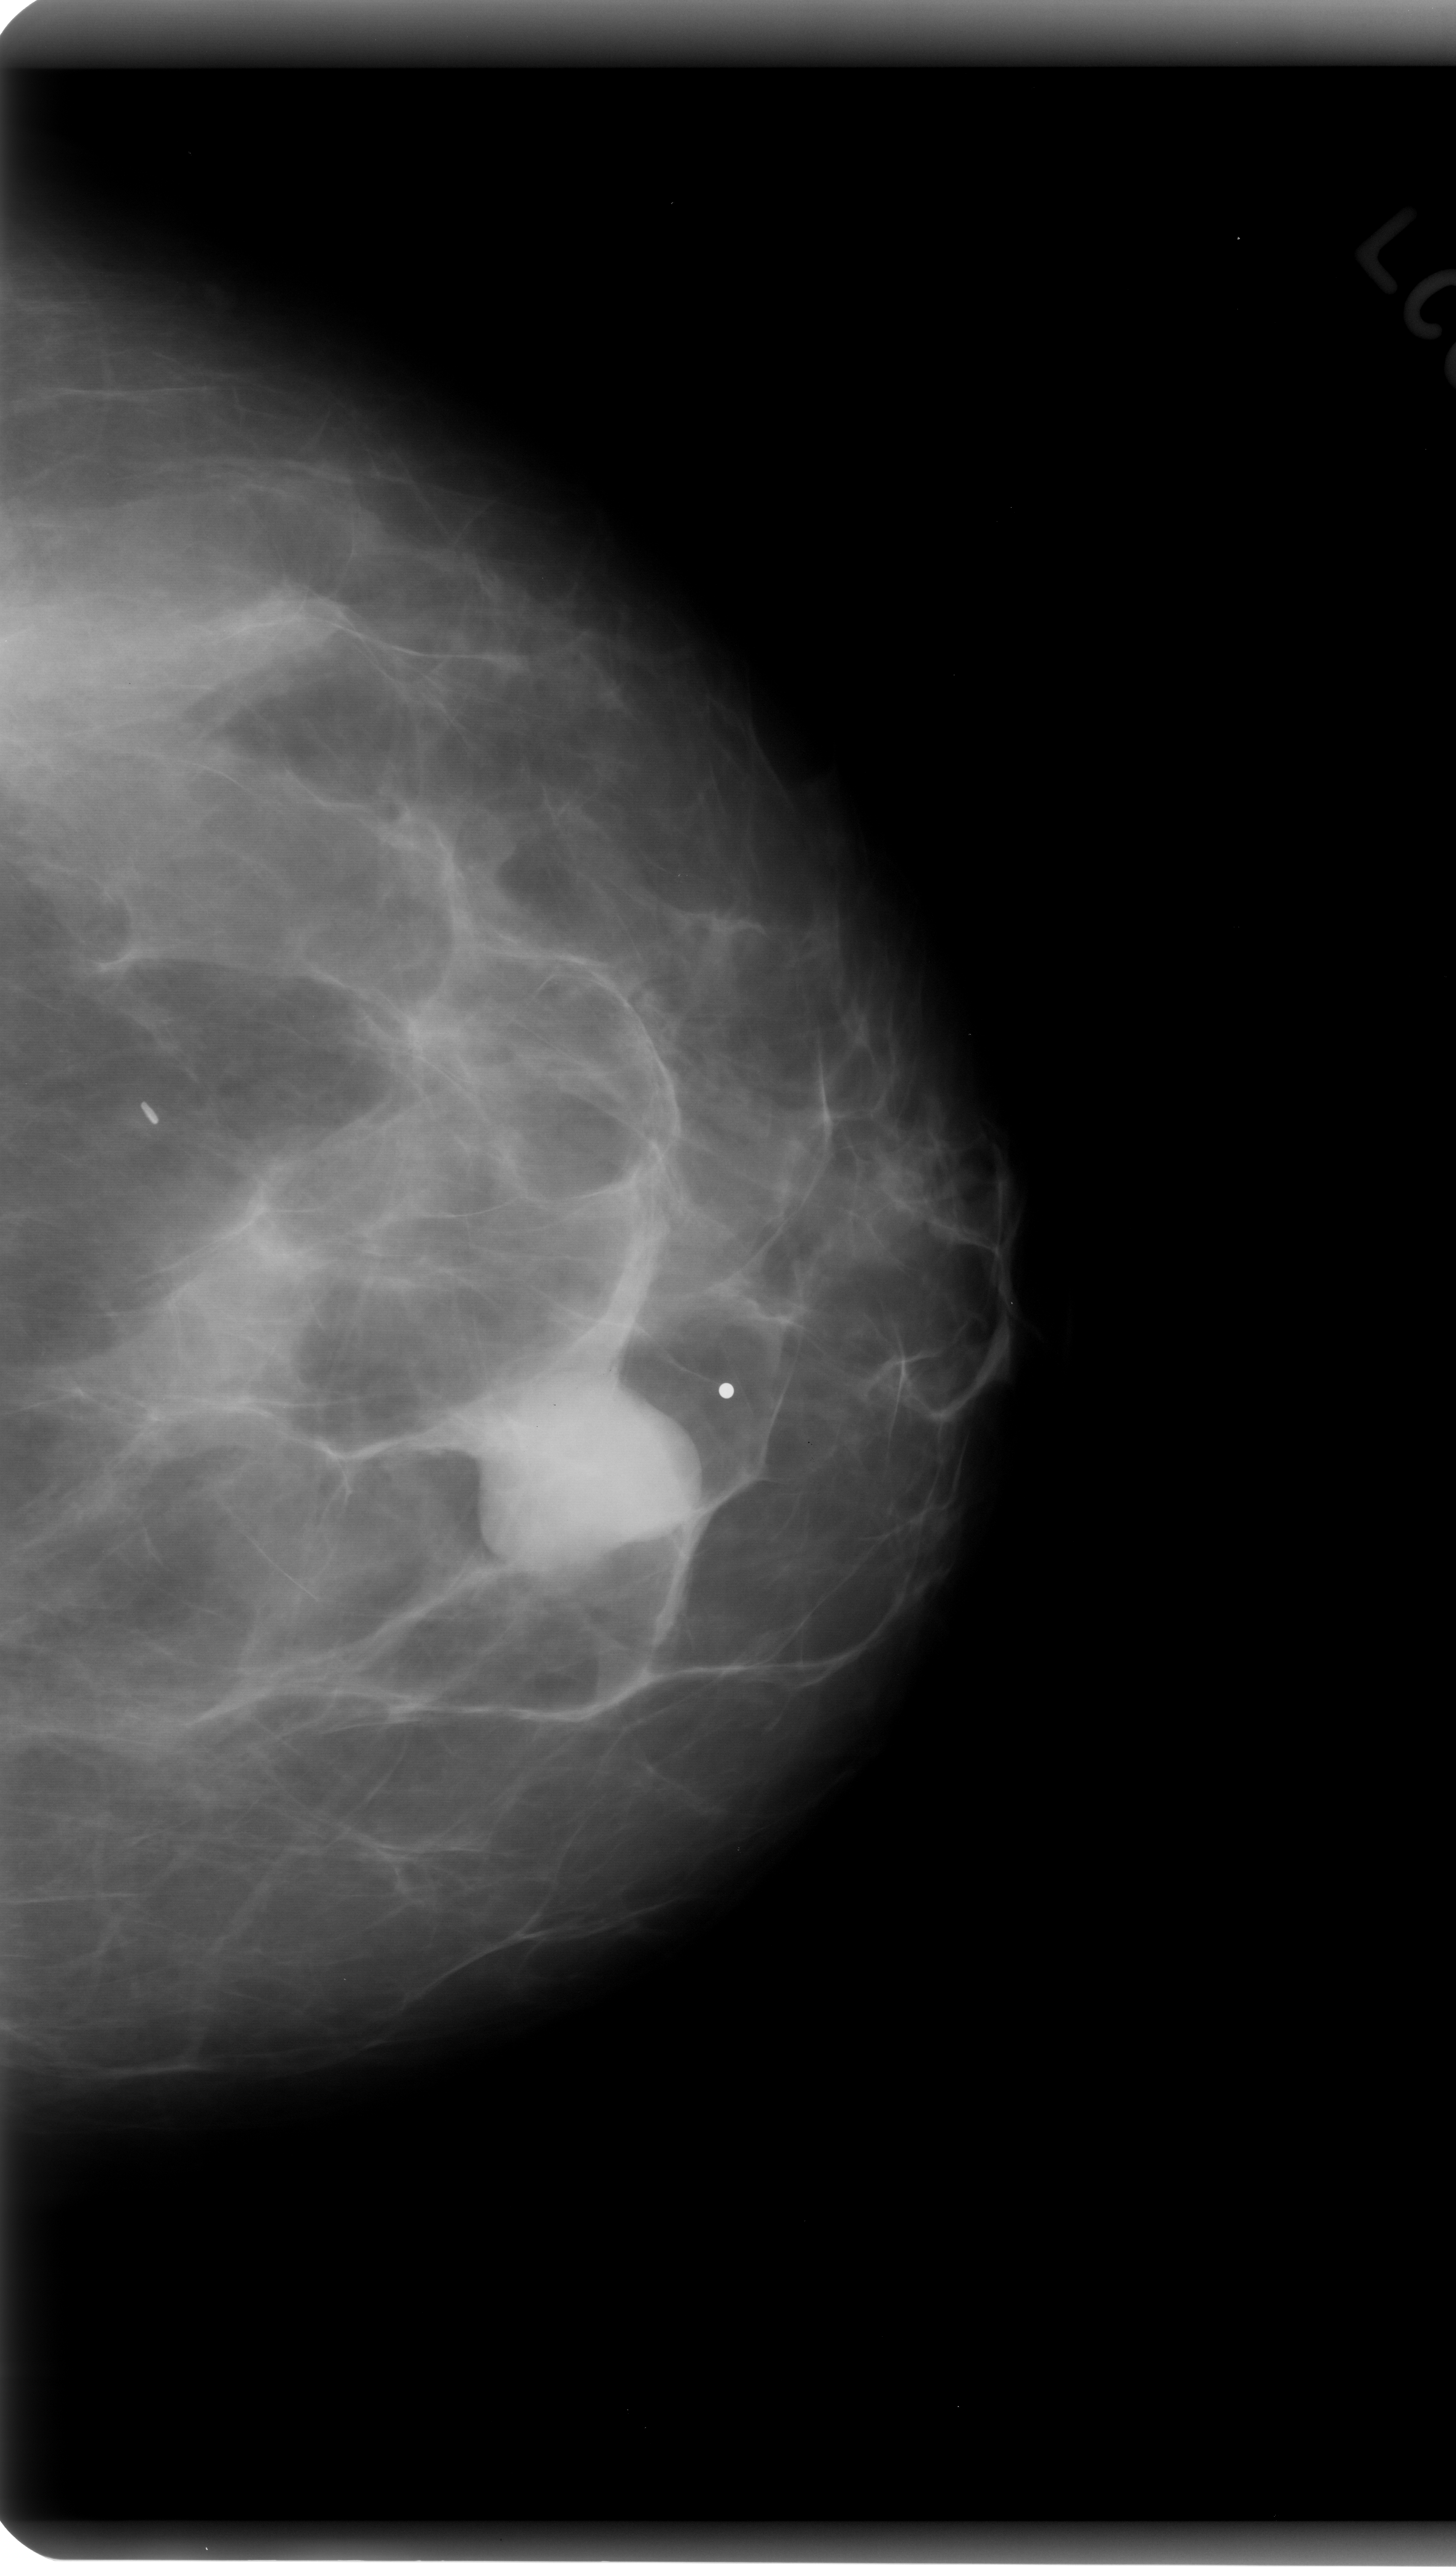
Digitized screen-film mammogram, left breast, CC view, BI-RADS breast density category 2 (scale 1–4).
Radiologist-marked abnormalities on this image: mass, shape oval, margins circumscribed; BI-RADS assessment category 4; subtlety rating 5 on a 1 (subtle) to 5 (obvious) scale; pathology result (as recorded, not read from the image): benign.